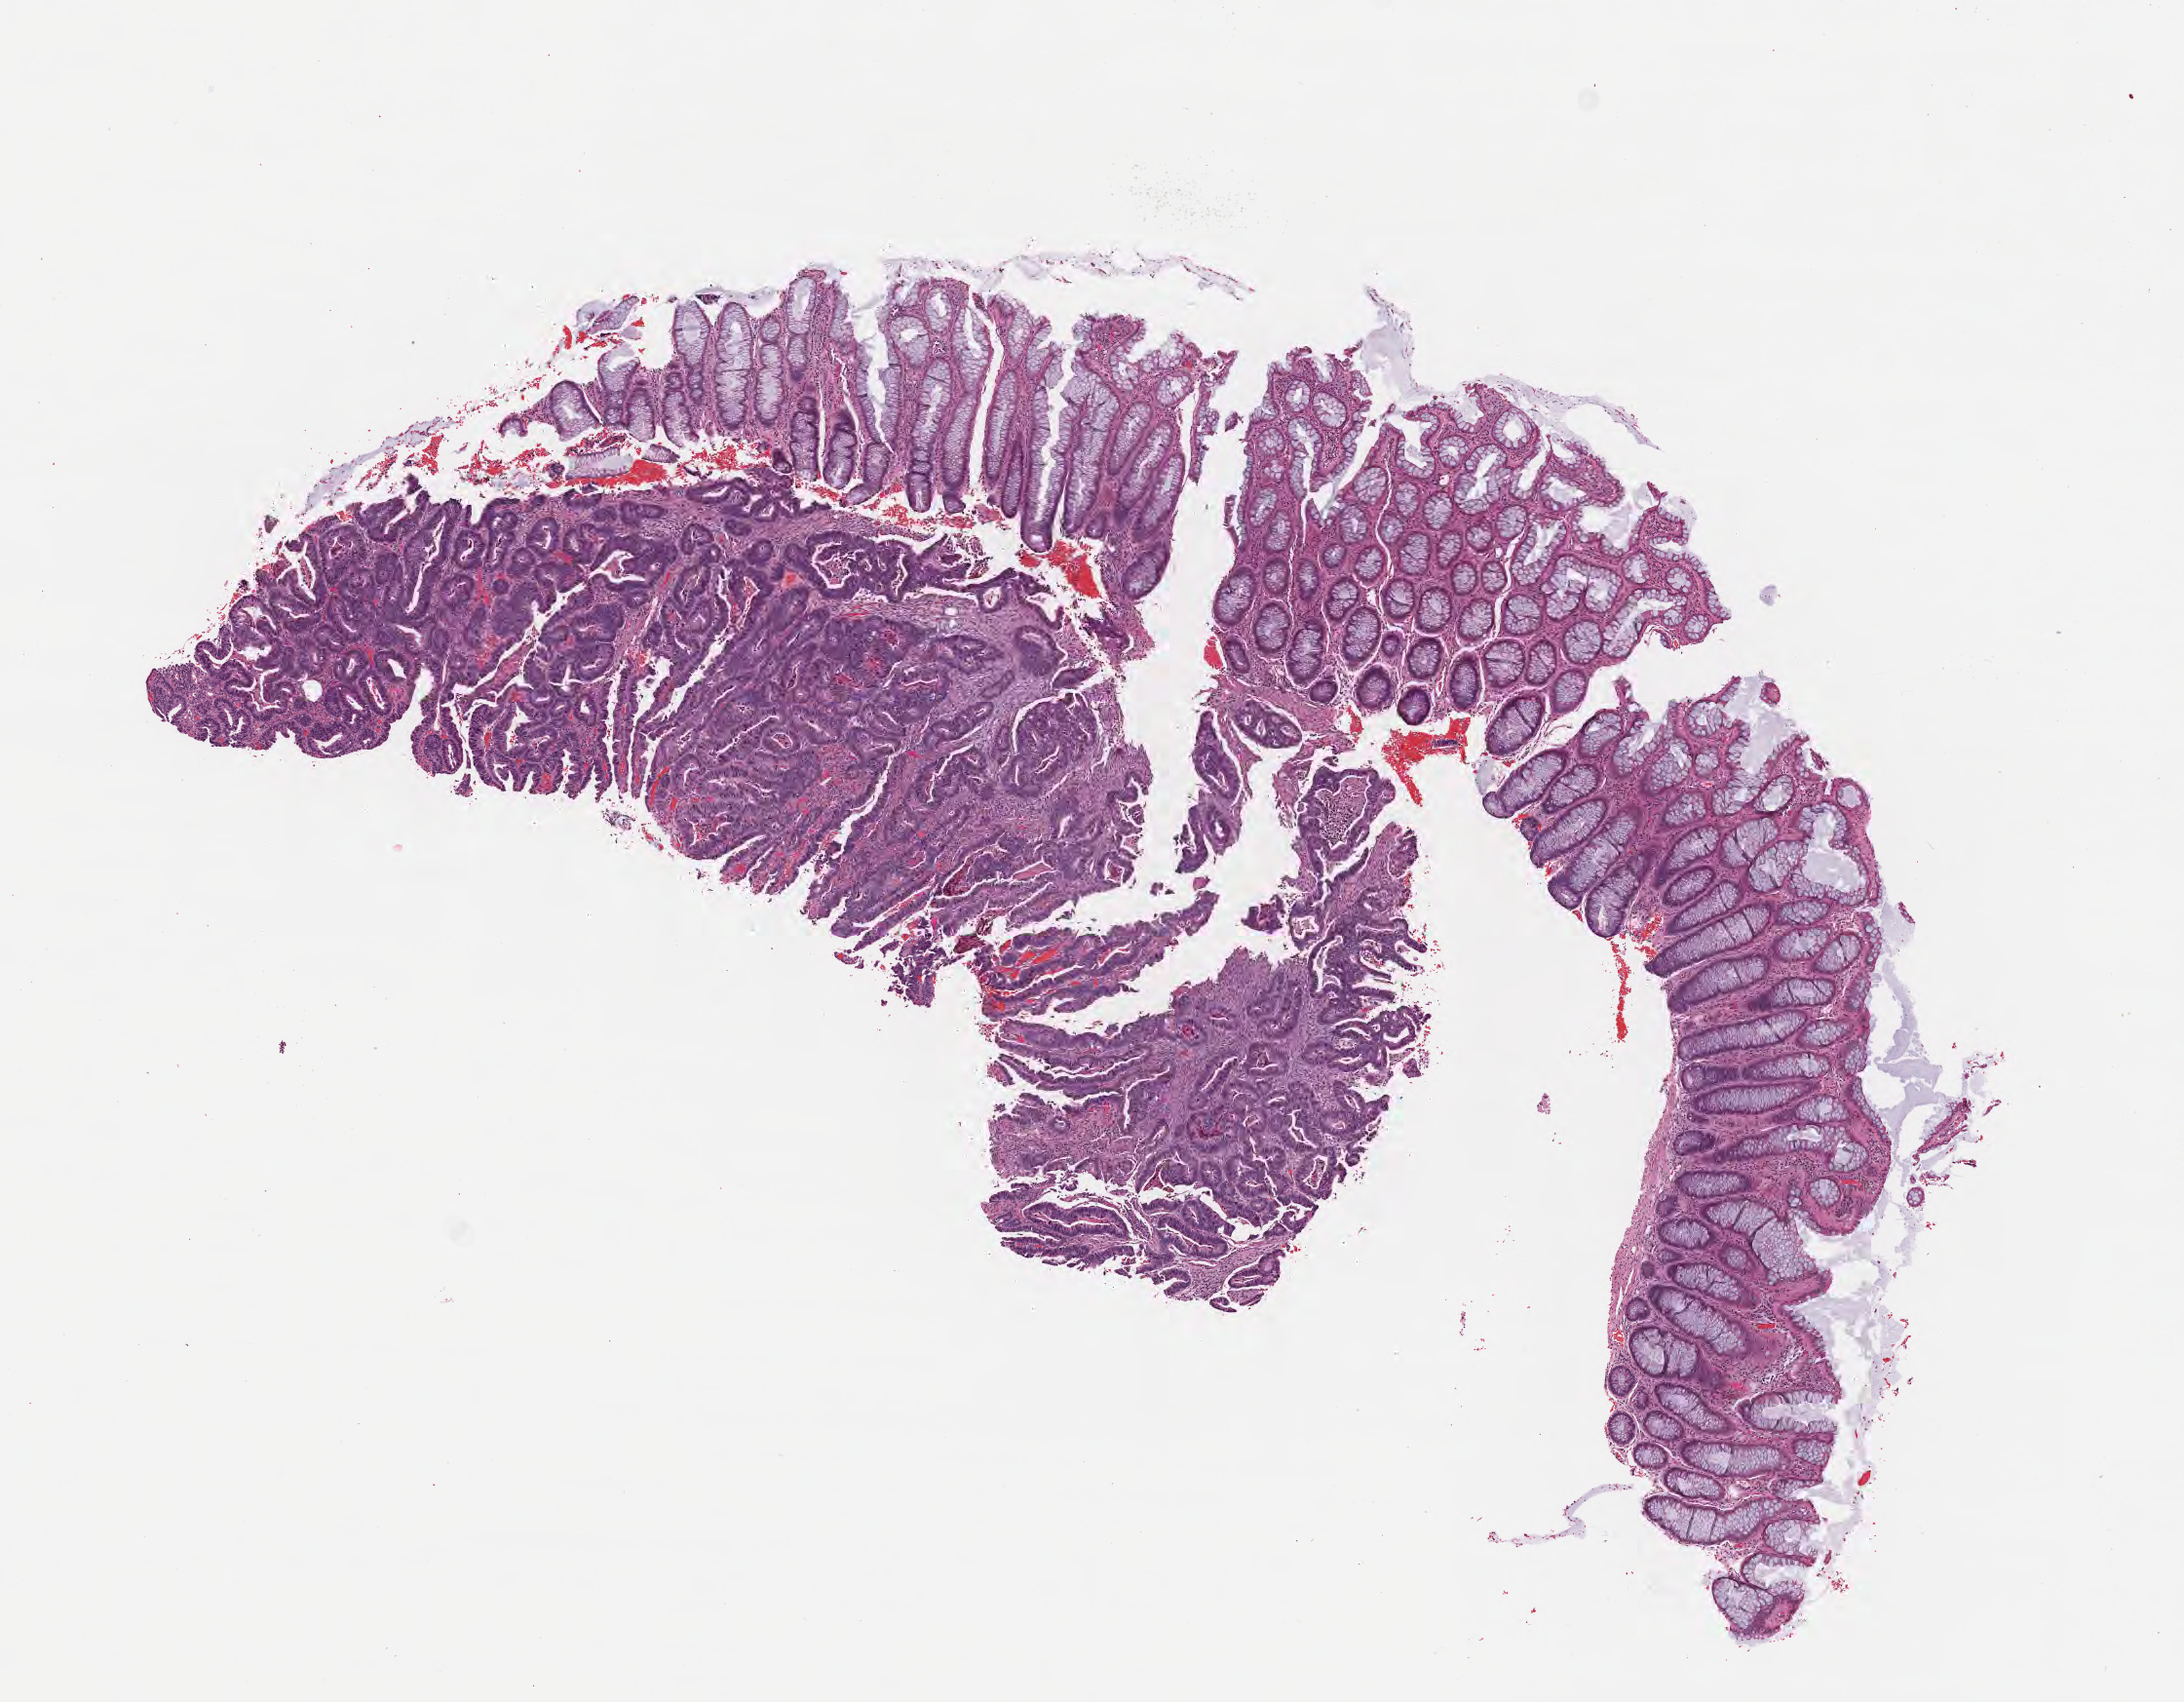
Haematoxylin and eosin whole-slide image — a low-resolution overview of the entire scanned area, about 9.1 x 7.1 mm, formalin-fixed, paraffin-embedded (FFPE) tissue, specimen: primary tumor, site: sigmoid colon. Male patient; age at initial diagnosis 50 years. Tumor grade: G2 (moderately differentiated). Pathologist review of this section (percent, as recorded): tumor cells 70%, tumor nuclei 70%, stromal cells 18%, necrosis 2%, normal cells 10%. Infiltration values recorded for this section: lymphocyte infiltration 4%, monocyte infiltration 2%, neutrophil infiltration 6%.
Diagnosis: Adenocarcinoma, NOS. AJCC pathologic stage: Stage IIIB. Section: top of the tissue portion.